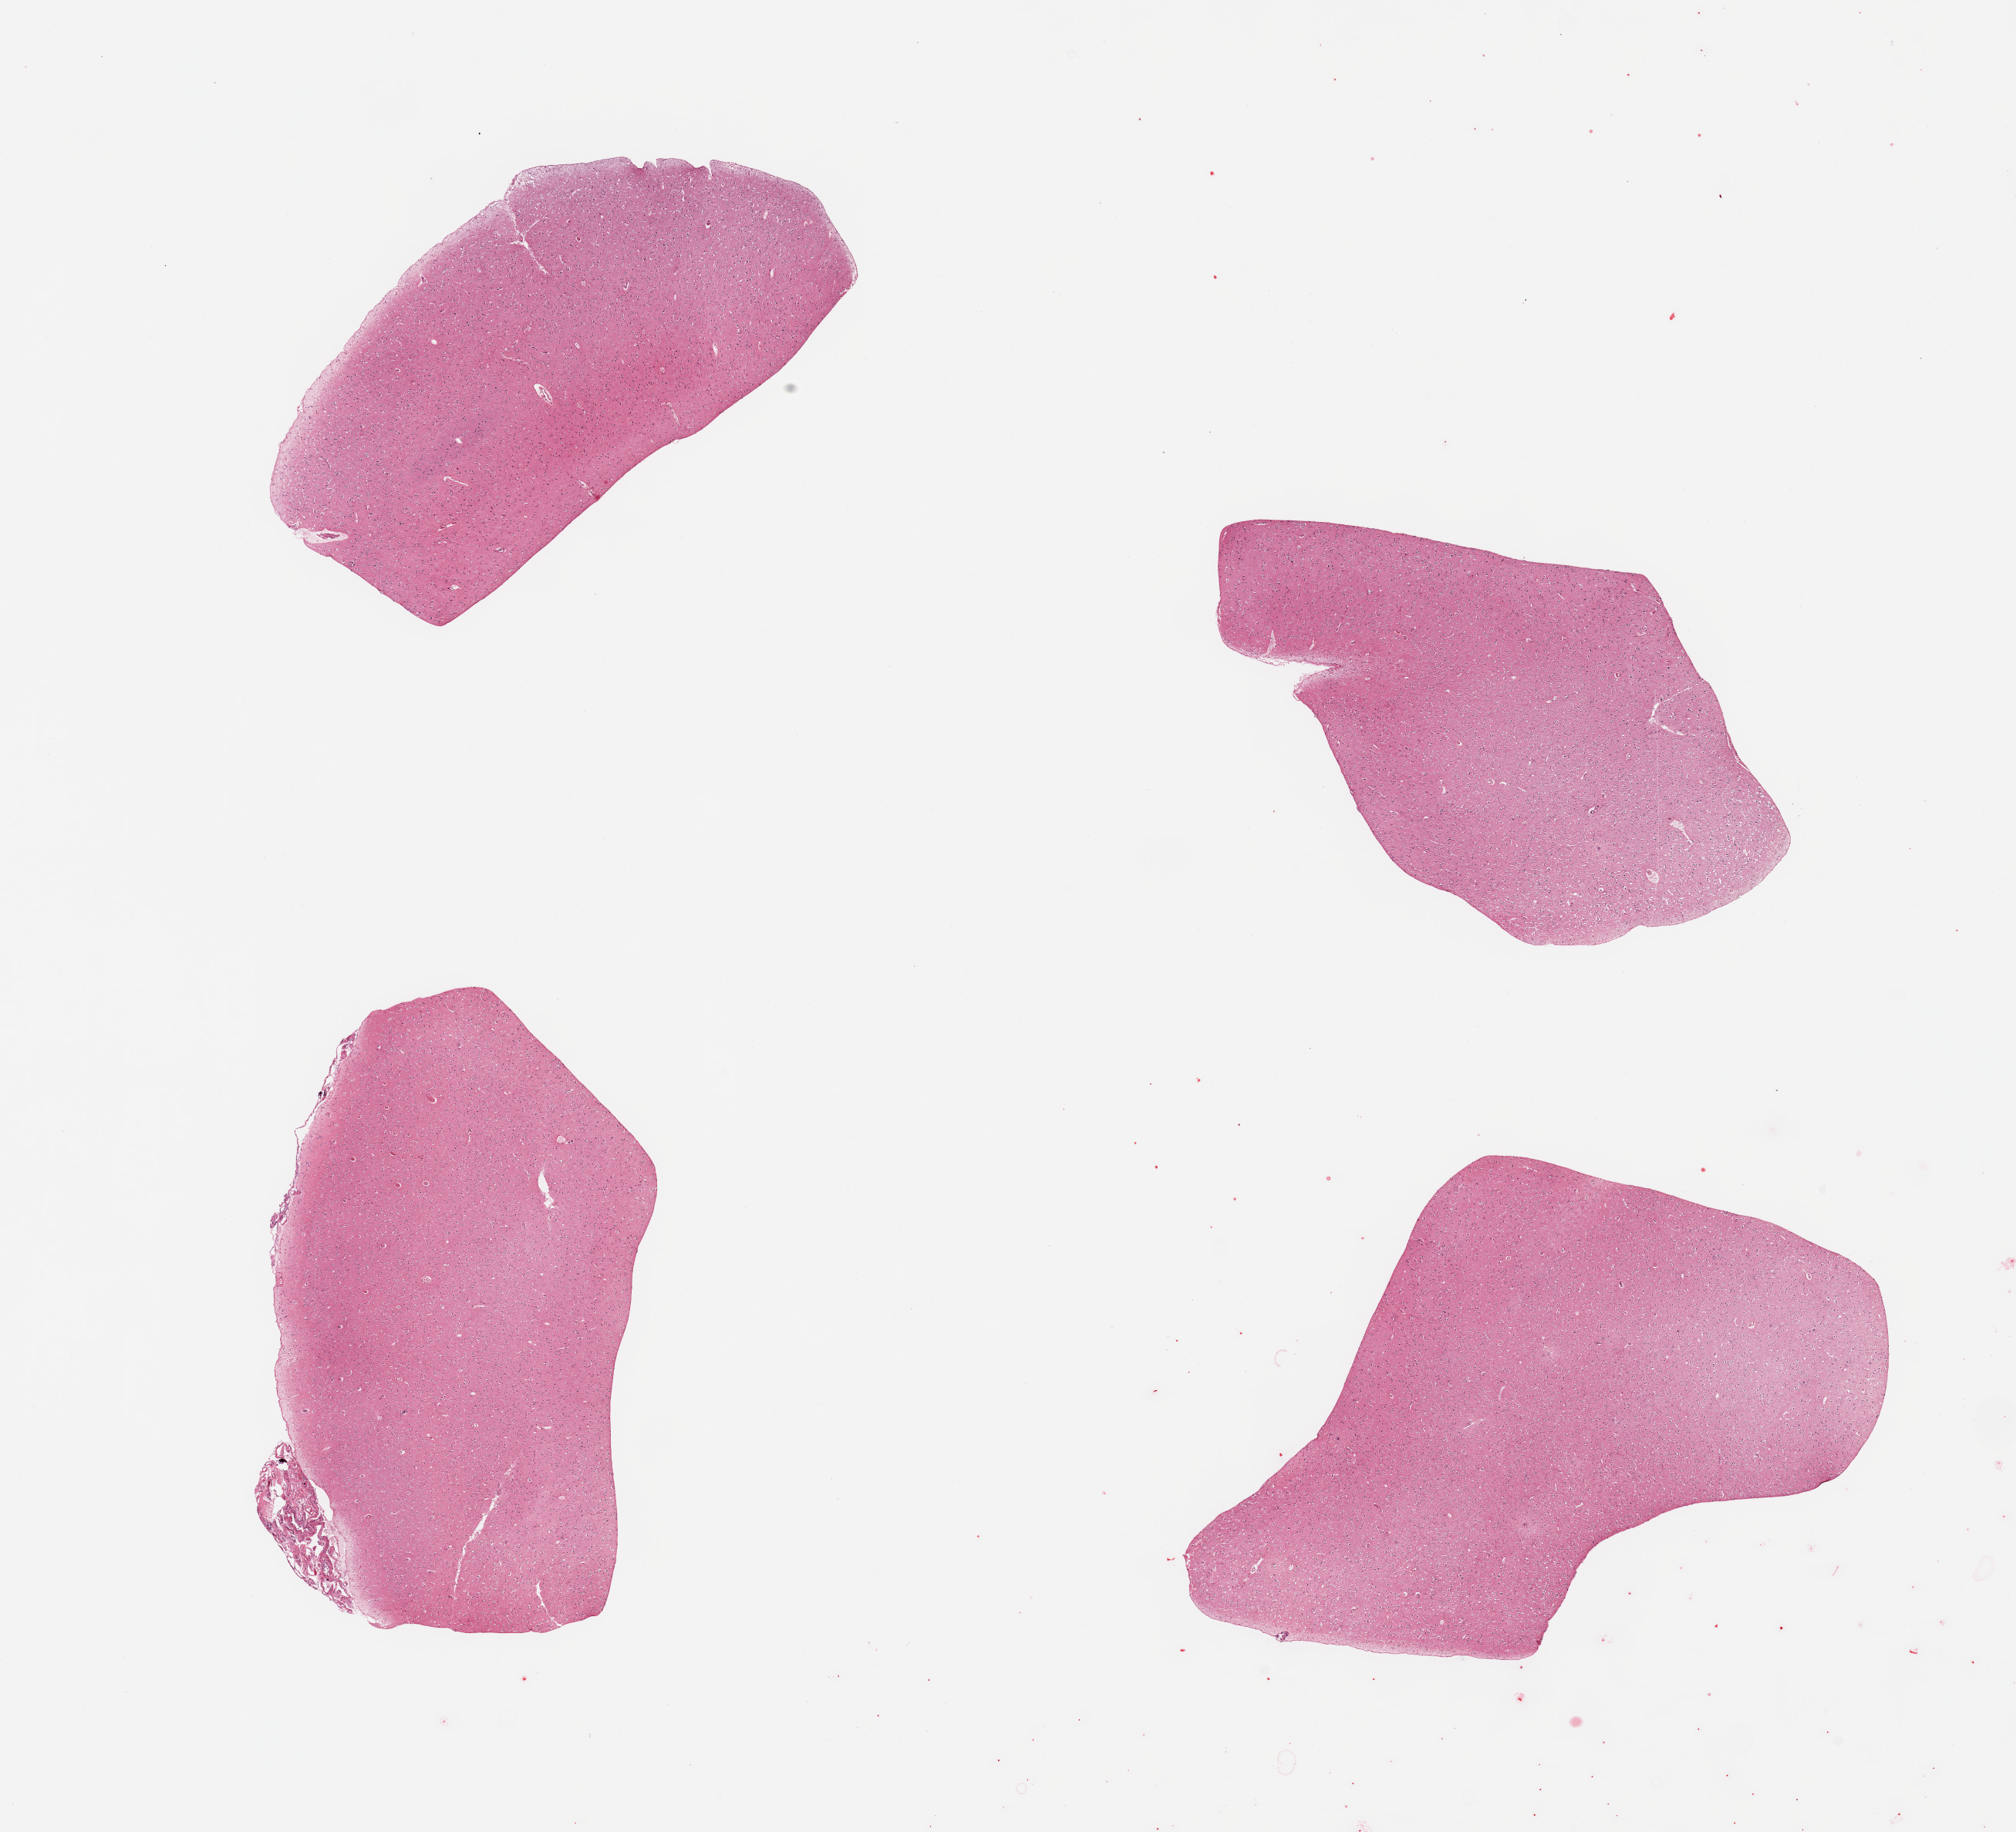
Digitized hematoxylin and eosin (H&E)-stained section — shown as a low-resolution overview of the whole scanned area (about 20.7 x 18.8 mm, acquisition: 20x scan), PAXgene-fixed, paraffin-embedded tissue, sampled site (target tissue): cerebral cortex, donor tissue sample.
Review note (as recorded): 4 pieces; one focus of attached meninges 1.9 mm.